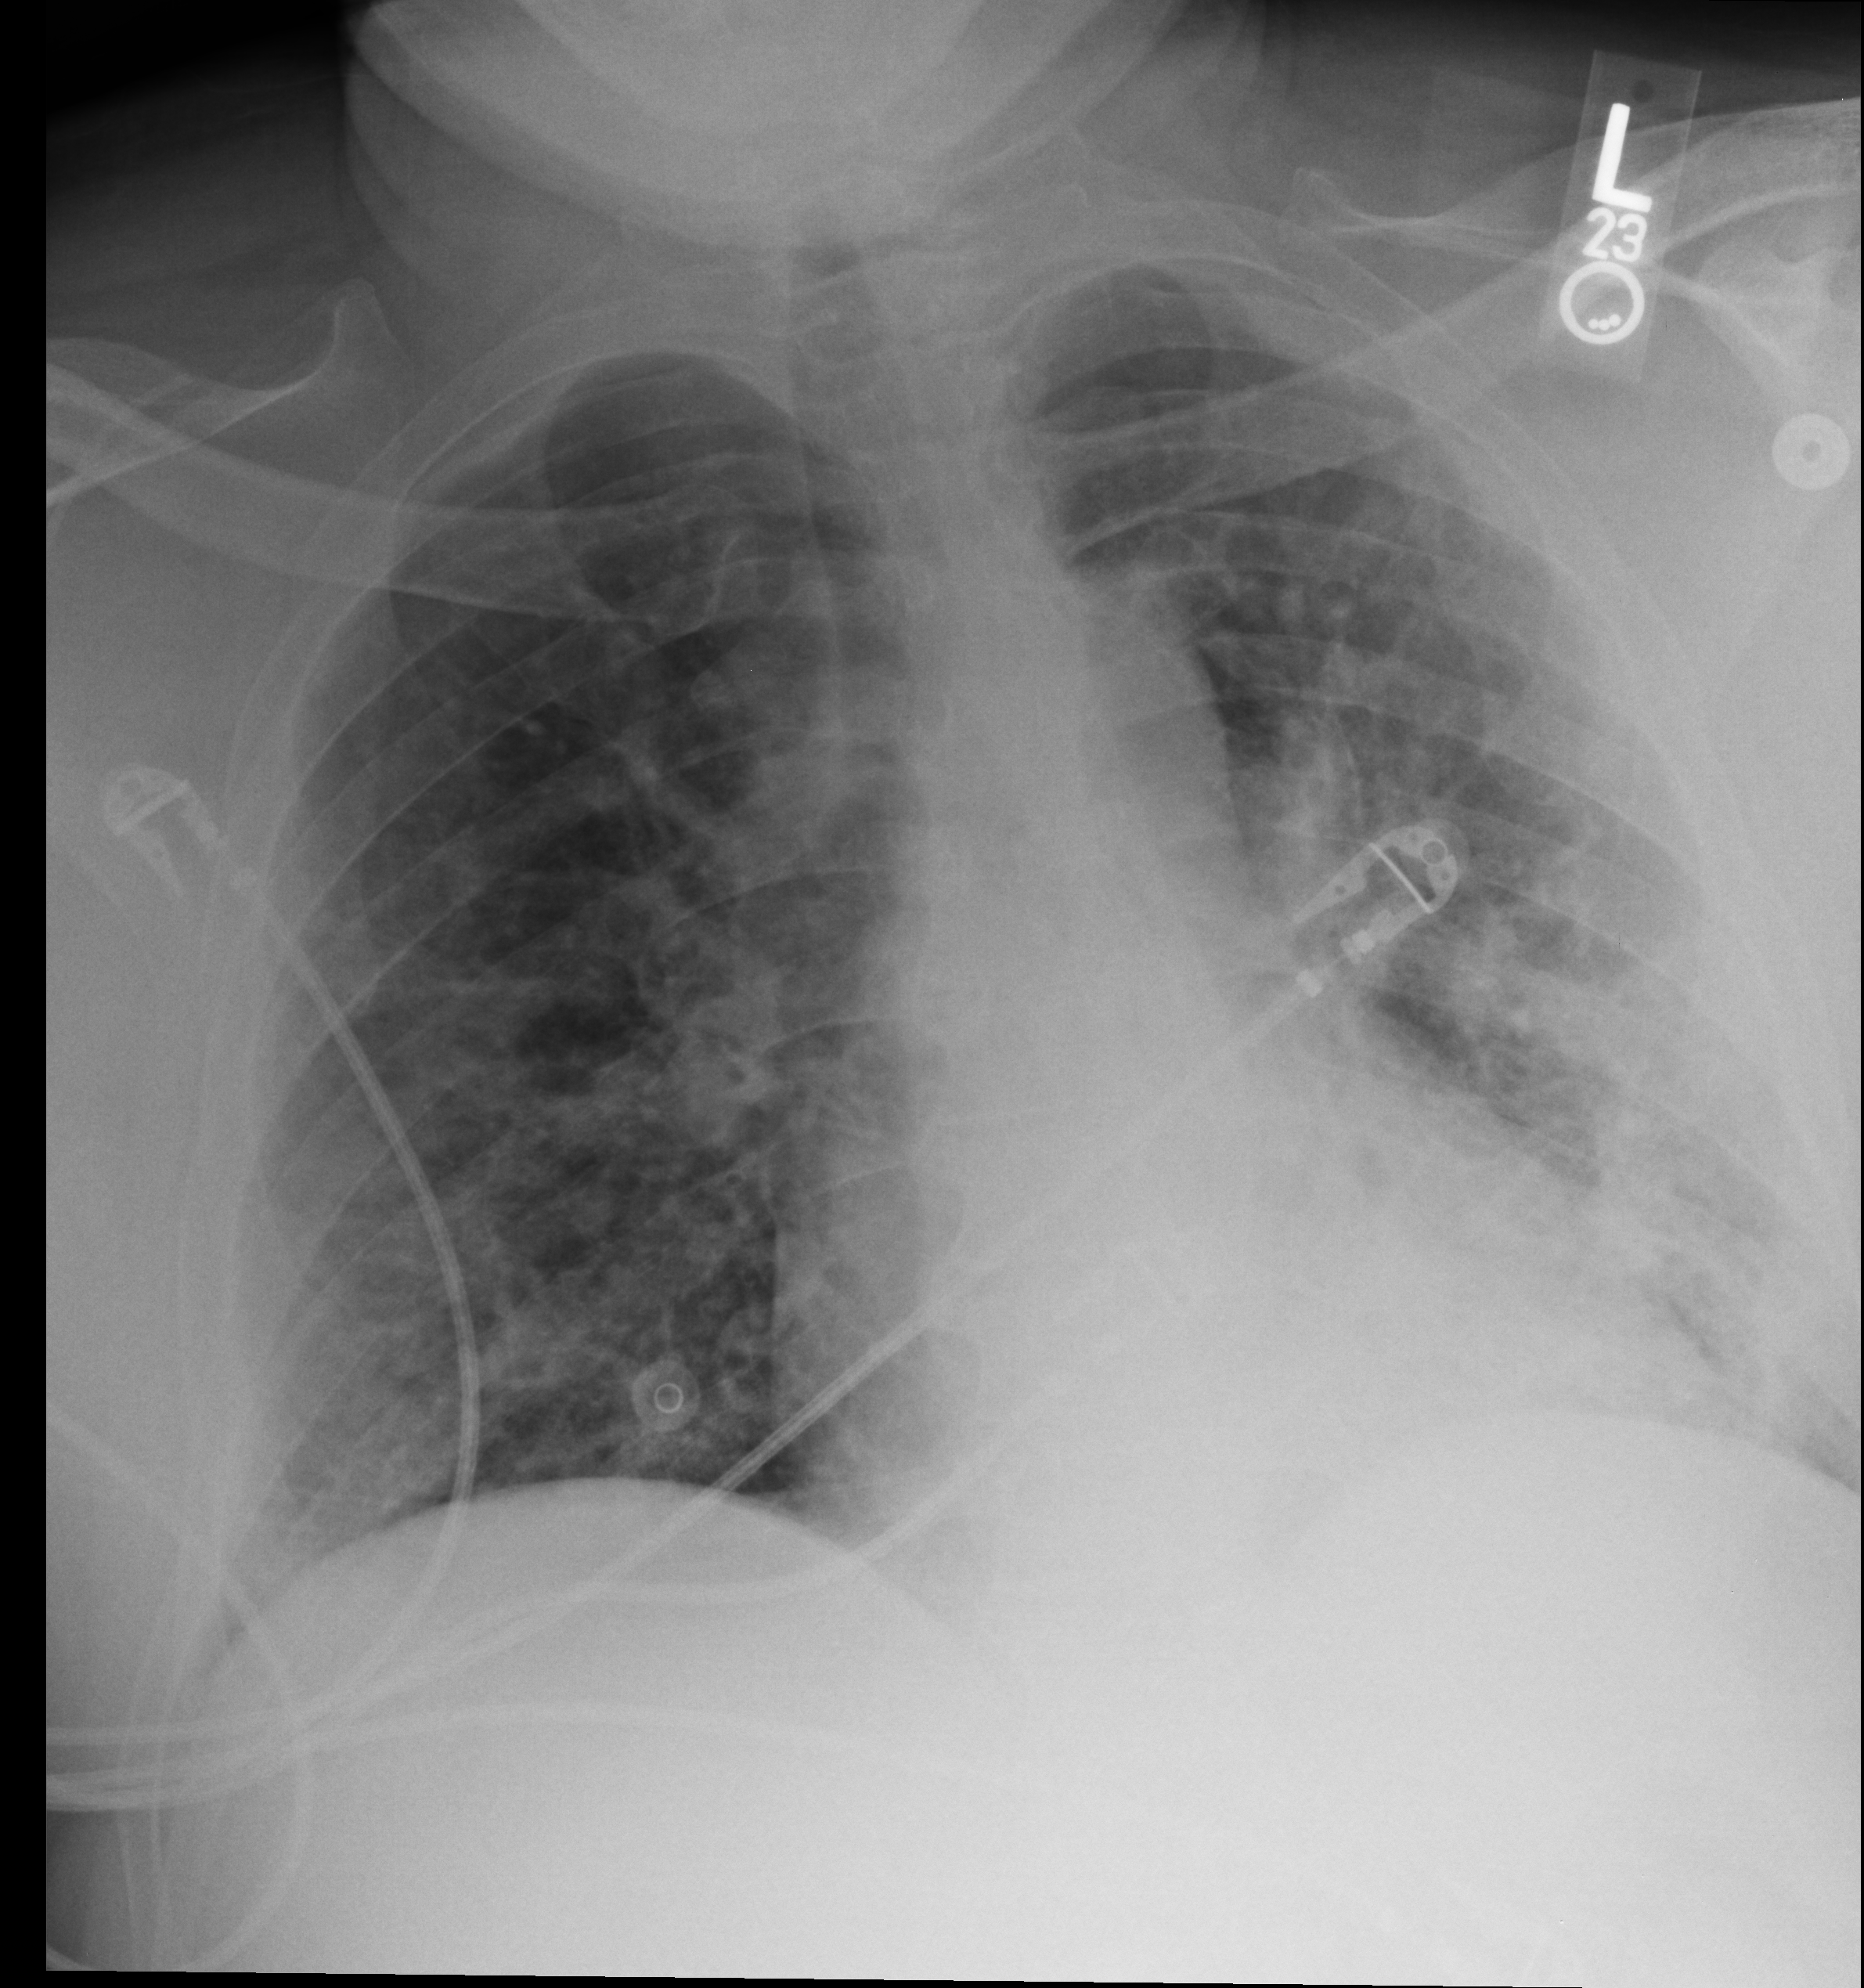
Bedside chest radiograph (computed radiography). Male patient hospitalised with COVID-19, age 18–59 years.
Admission-level facts for this patient (not findings on this image; timing relative to this image not recorded): chronic kidney disease (admission record): no.